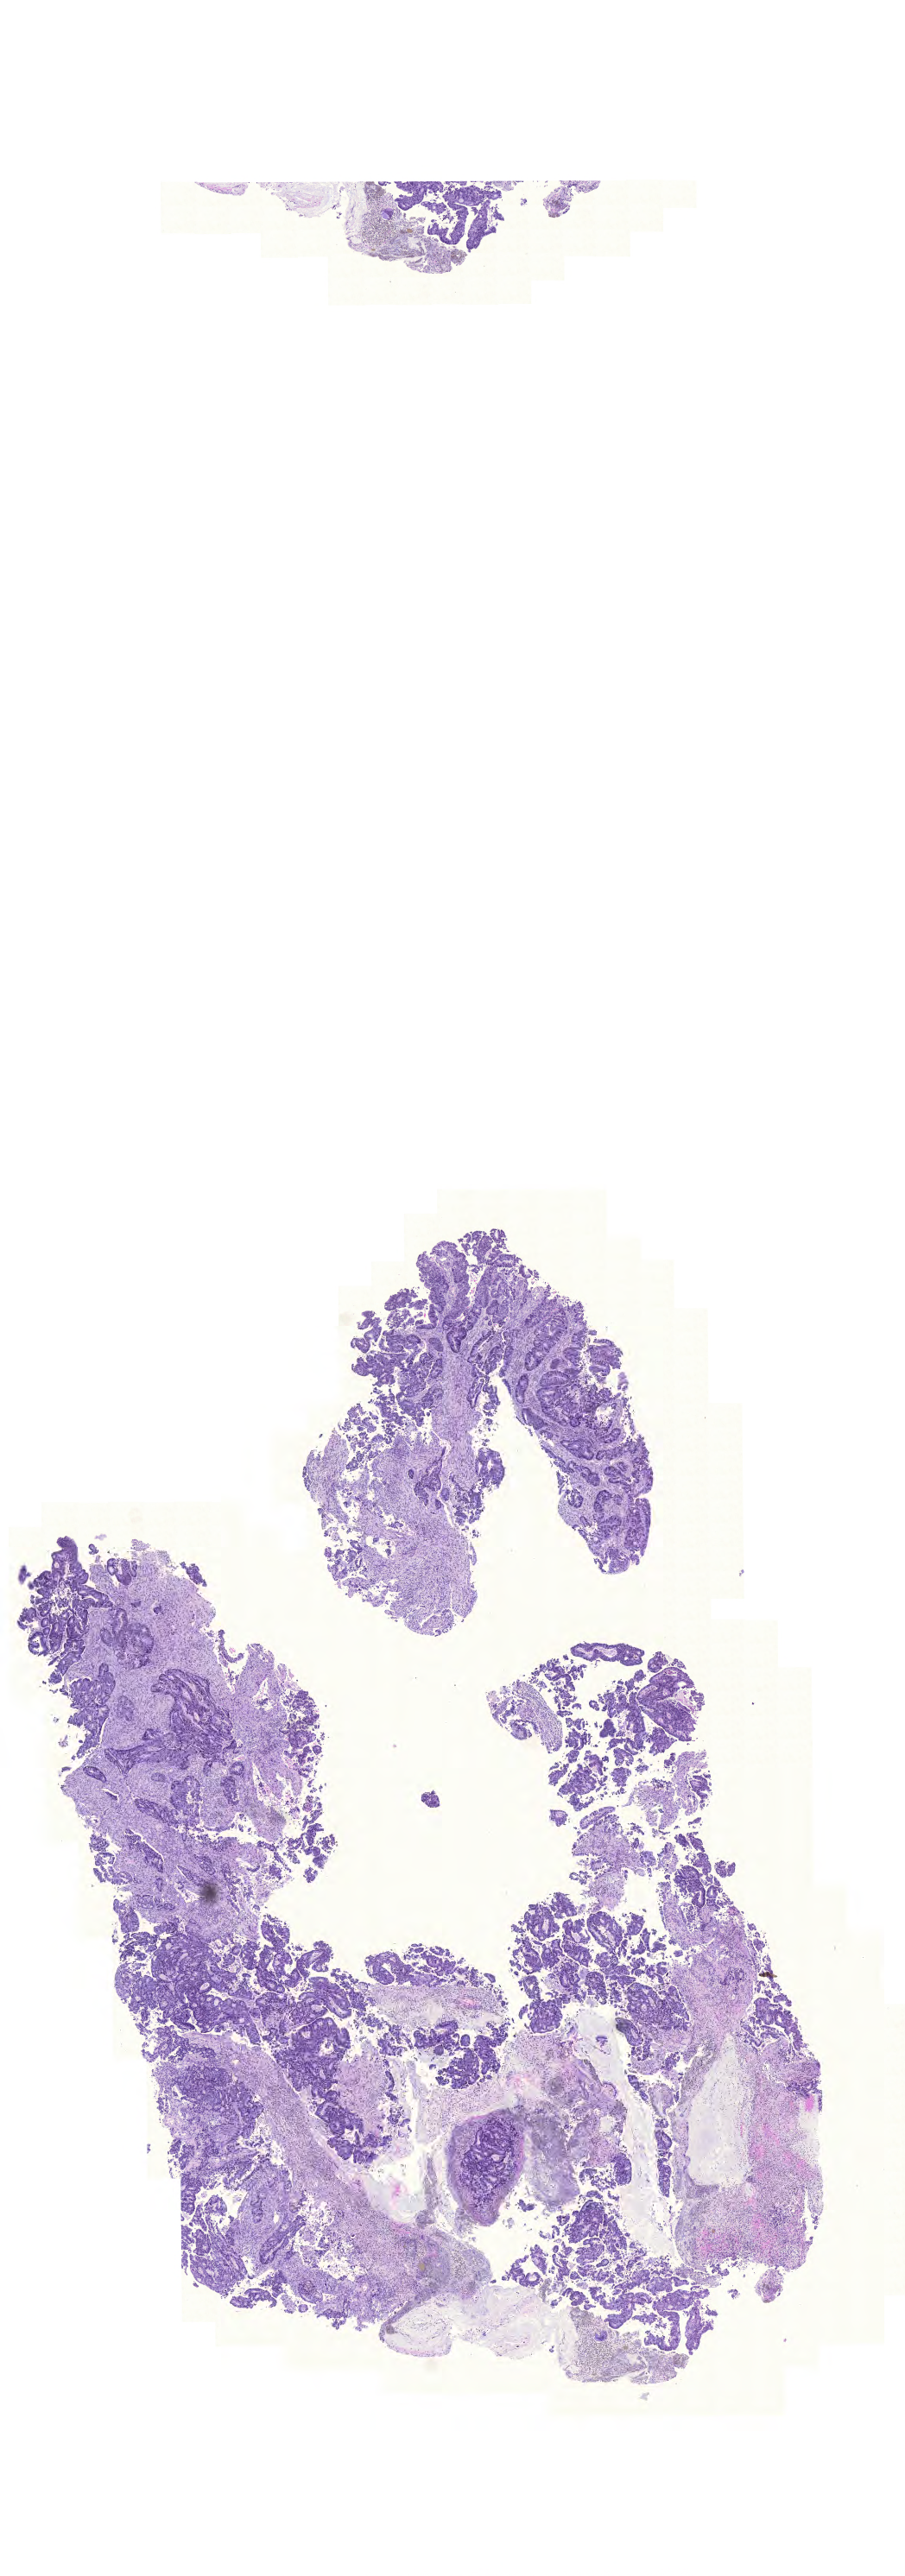
Whole-slide histology image, Hematoxylin and eosin (H&E) stained, whole scanned area (about 7.8 x 22.2 mm, from a 20x scan) shown as a low-resolution overview, formalin-fixed paraffin-embedded (FFPE) diagnostic section, colon, primary tumour sample. Female, age 55 years at initial diagnosis.
Diagnosis: Adenocarcinoma, NOS (sigmoid colon). AJCC pathologic stage: I (6th edition). Lymph nodes positive (case pathology): 0 of 19 examined.